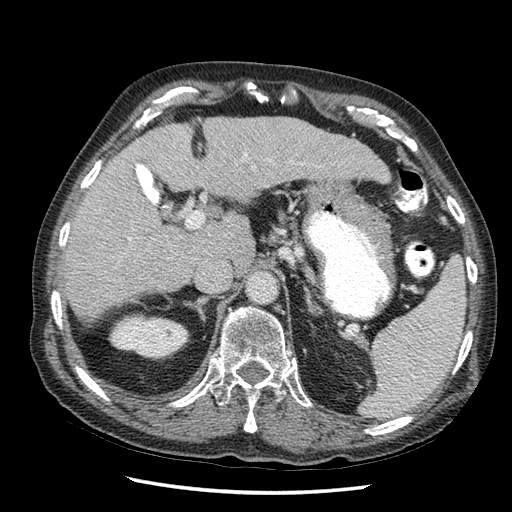
Contrast-enhanced abdominal CT (liver protocol), one axial slice; slice 27 of 67 in the series (ordered by position); reconstruction kernel STANDARD; 120 kVp; soft-tissue window (W 400 / L 40 HU); 2.5 mm slice thickness; 512 × 512 image matrix. Case-level facts recorded for this patient, not image findings: diagnosis: hepatocellular carcinoma (patient treated with transarterial chemoembolisation; whether this scan precedes or follows treatment is not stated here); TNM stage (as recorded): Stage-I; Child-Pugh class: A; tumour nodularity: uninodular.
Annotated regions visible in this slice (semi-automatic segmentation, software-assisted and operator-edited):
- liver parenchyma outside the tumour (the mass and vessels are separate outlines, so this box may not span the whole liver): bounding box (x1, y1, x2, y2) in pixels: (60, 118, 383, 316)
- liver vessels: (131, 149, 246, 241)